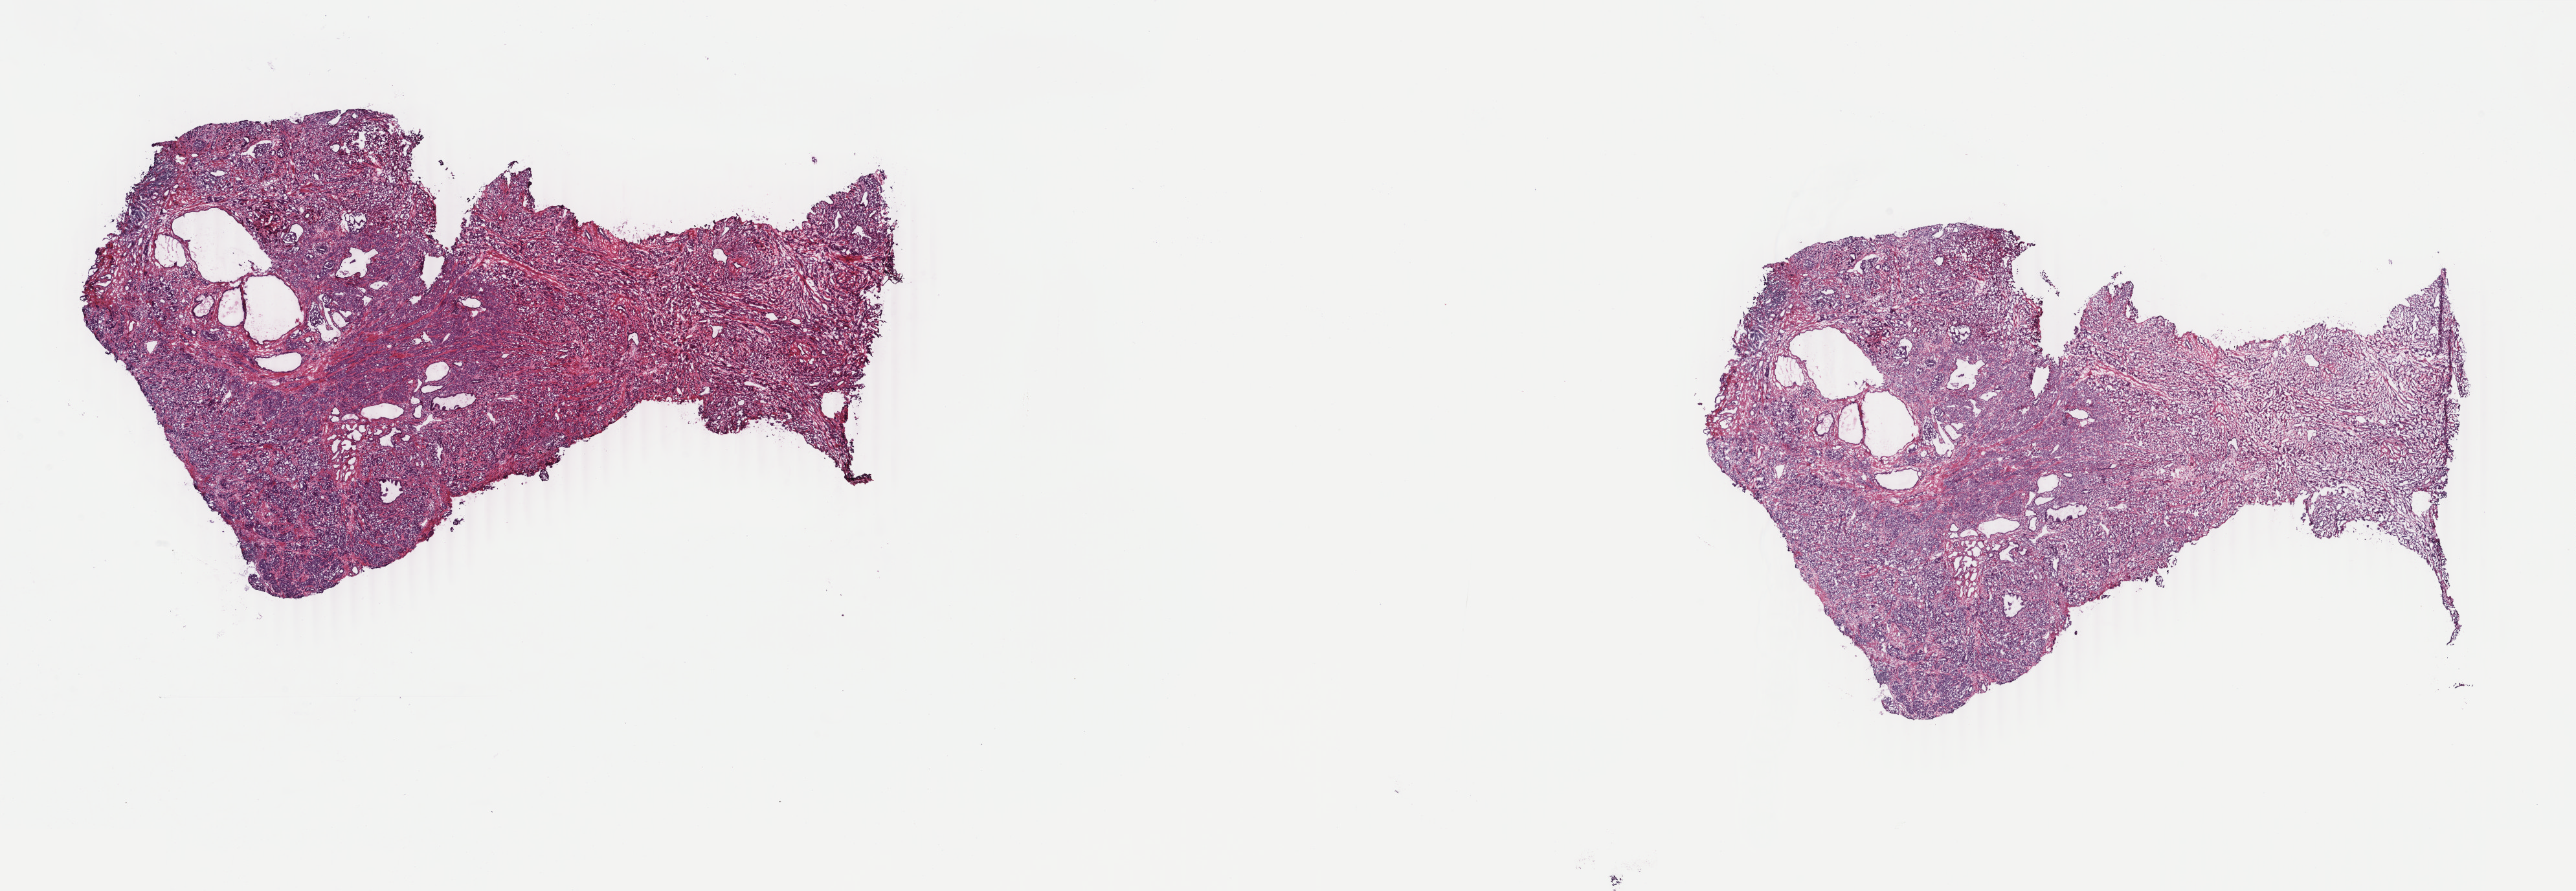
Hematoxylin and eosin (H&E) stained whole-slide image, shown as a low-resolution overview of the whole scanned area (about 31.6 x 10.9 mm); frozen section; prostate, primary tumour sample. Male patient; age at initial diagnosis 54 years. Gleason score: 9 (4+5). Pathologist review of this section (percent, as recorded): tumour cells 90%, tumour nuclei 95%, normal cells 10%, stromal cells 0%, necrosis 0%. Infiltration values recorded for this section: lymphocyte infiltration 0%, monocyte infiltration 0%, neutrophil infiltration 0%.
* laterality: bilateral
* lymph nodes positive (case pathology): 3 of 12 examined
* diagnosis: Adenocarcinoma, NOS (prostate gland)